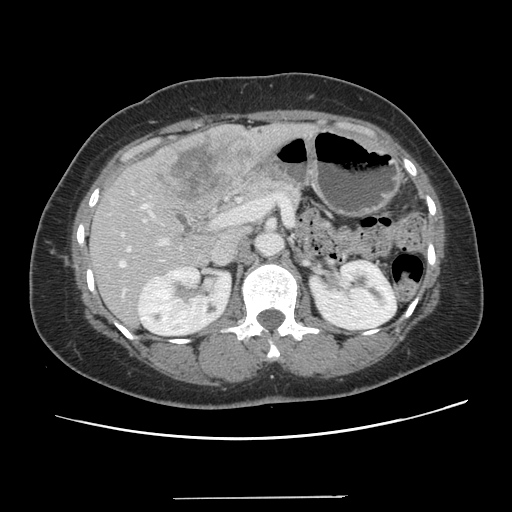
Contrast-enhanced abdominal CT, one axial slice; position 66 of 141 along the scan axis; 120 kVp; intravenous contrast given; soft-tissue window (W 400 / L 40 HU); 2.5 mm slice thickness; 512 × 512 image matrix. Female patient, age 53 years. From the clinical record (not read from this slice): diagnosis: colorectal cancer liver metastases, imaged before liver resection; multiple liver metastases: no; largest metastasis: 14.5 cm; disease in both lobes: yes.
Annotated regions visible in this slice (outlined manually by an expert reader):
- hepatic veins: bounding box (x1, y1, x2, y2) in pixels: (119, 247, 129, 266)
- liver: (91, 124, 304, 326)
- planned liver remnant (the part of the liver to remain after resection): (90, 211, 242, 328)
- portal vein (with intrahepatic branches): (122, 204, 167, 244)
- liver metastasis: (152, 132, 260, 202)